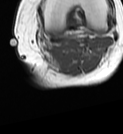
MRI of an extremity soft-tissue mass, one axial slice; MR volume resampled by the dataset authors to the PET/CT grid (not the native acquisition matrix); 3.27 mm slice thickness; 123 × 134 image matrix, field of view 120 × 131 mm. Female patient. Case-level facts recorded for this patient, not image findings: histological type: extraskeletal high grade osteogenic sarcoma; grade: high; site of the primary tumour: left calf.
Outlined on this slice (expert contour drawn on MRI and transferred to this co-registered scan by the dataset authors):
- gross tumour volume (mass): bounding box <51,46,62,58> (left, top, right, bottom; pixels)